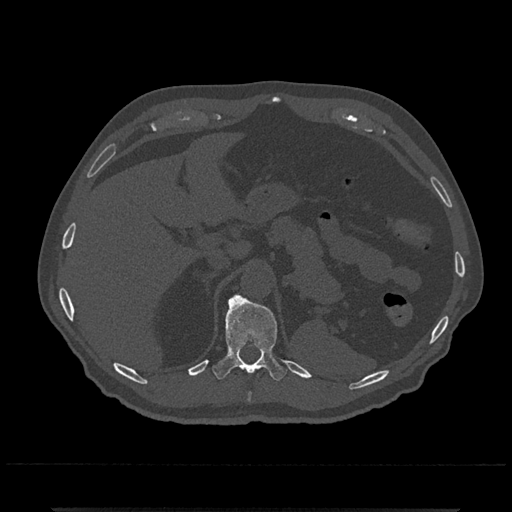
CT including the spine, one axial slice; slice 498 of 797 in the series (ordered by position); 120 kVp; bone window (W 1800 / L 400 HU); 512 × 512 image matrix. Patient: male, 67 years. From the clinical record (not read from this slice): primary cancer: prostate.
Outlined on this slice (semi-automatic segmentation, software-assisted and operator-edited):
- T10 vertebra: bounding box <249,393,251,398> (left, top, right, bottom; pixels)
- T11 vertebra: <212,293,287,382>